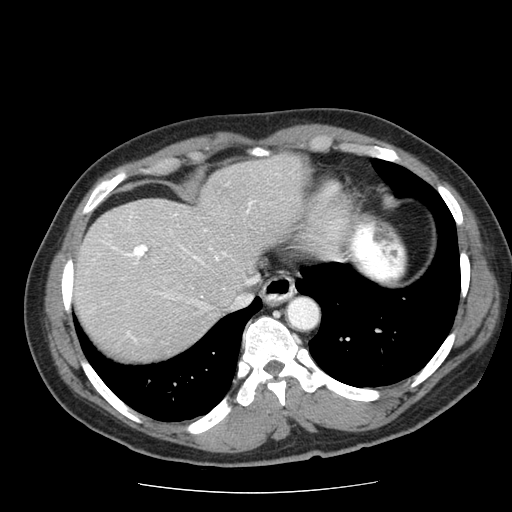
Contrast-enhanced abdominal CT (liver protocol), one axial slice; position 56 of 85 along the scan axis; 120 kVp; soft-tissue window (W 400 / L 40 HU); 512 × 512 image matrix. From the clinical record (not read from this slice): diagnosis: hepatocellular carcinoma (patient treated with transarterial chemoembolisation; whether this scan precedes or follows treatment is not stated here); TNM stage (as recorded): Stage-IIIA; Child-Pugh class: A; tumour differentiation: well differentiated; tumour nodularity: multinodular.
Outlined on this slice (semi-automatically segmented with operator editing):
- liver parenchyma outside the tumour (the mass and vessels are separate outlines, so this box may not span the whole liver): bounding box (x1, y1, x2, y2) in pixels: (72, 154, 304, 360)
- liver vessels: (103, 201, 253, 341)